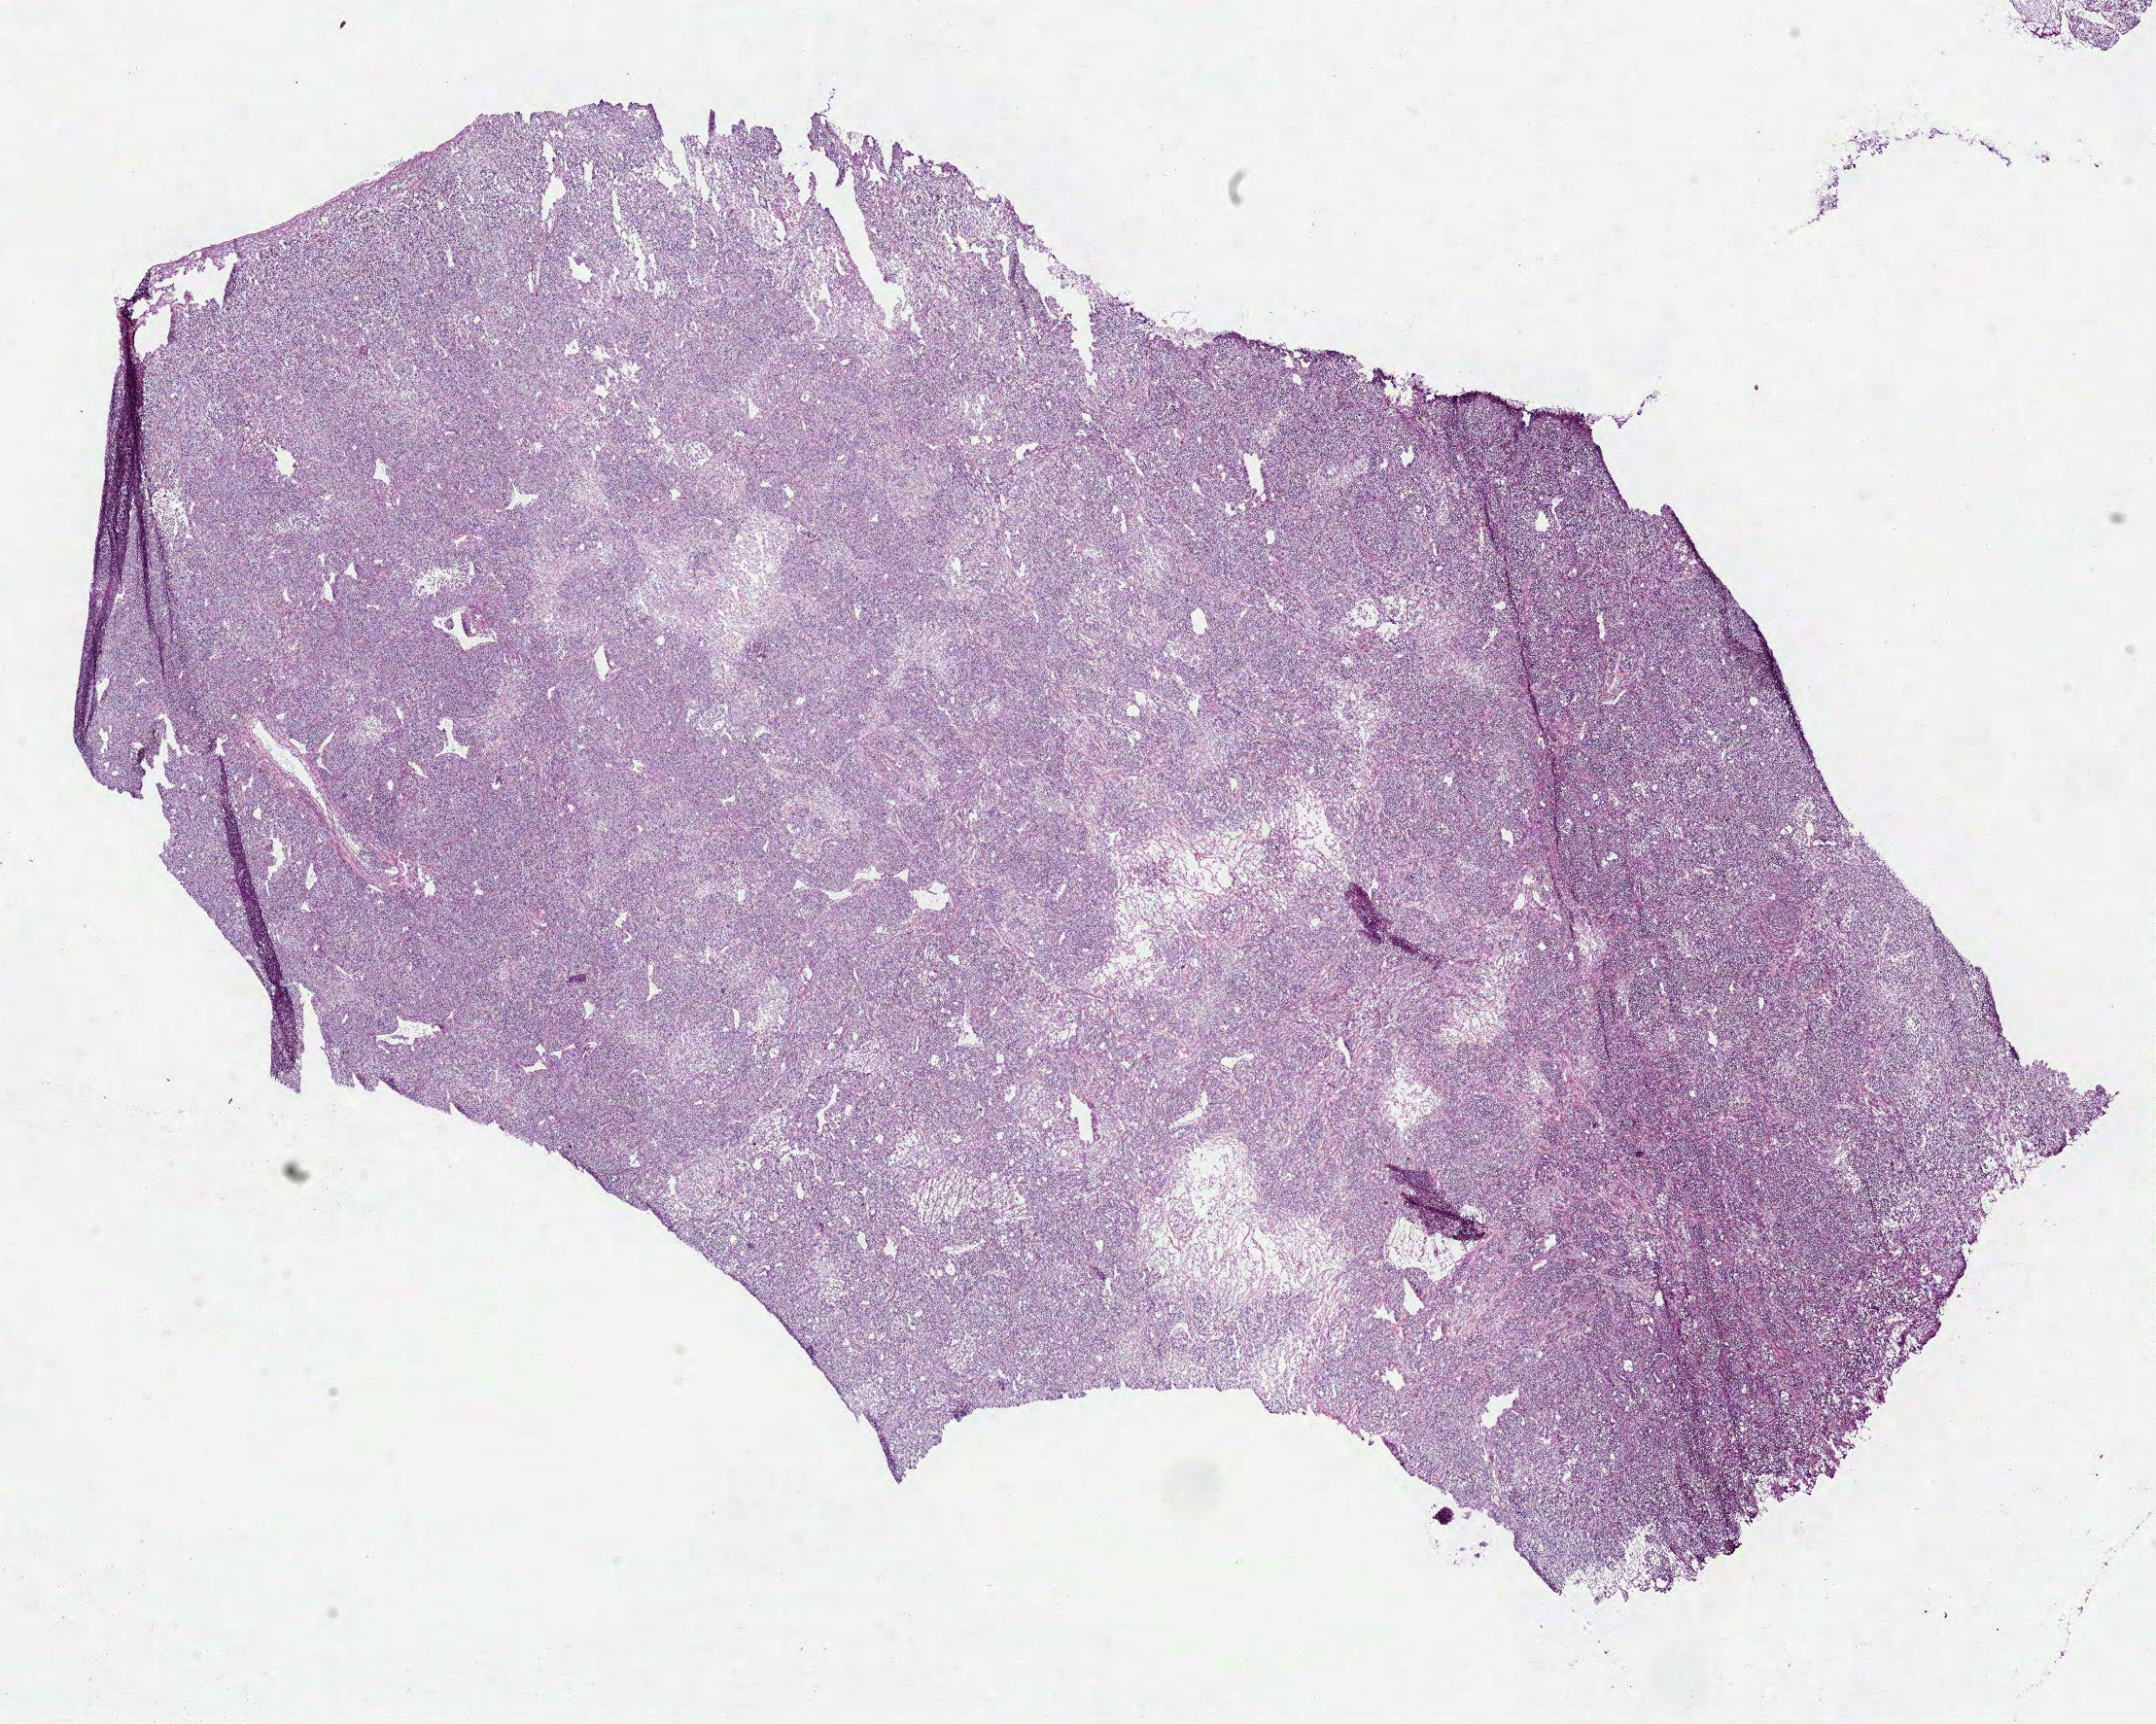
Digitized H&E tissue section (whole slide), a low-resolution overview of the entire scanned area, about 17.9 x 14.3 mm (slide scanned at 40x). Frozen section from the bottom of the tissue portion. Sample: primary tumour, lung. Female, age 69 years at initial diagnosis. Composition of this section per pathologist review: tumour cells 80%, tumour nuclei 85%, normal cells 0%, stromal cells 10%, necrosis 10%.
Histologic diagnosis: Bronchiolo-alveolar adenocarcinoma, NOS (upper lobe, lung). Laterality: left. AJCC pathologic stage: IA (7th edition).